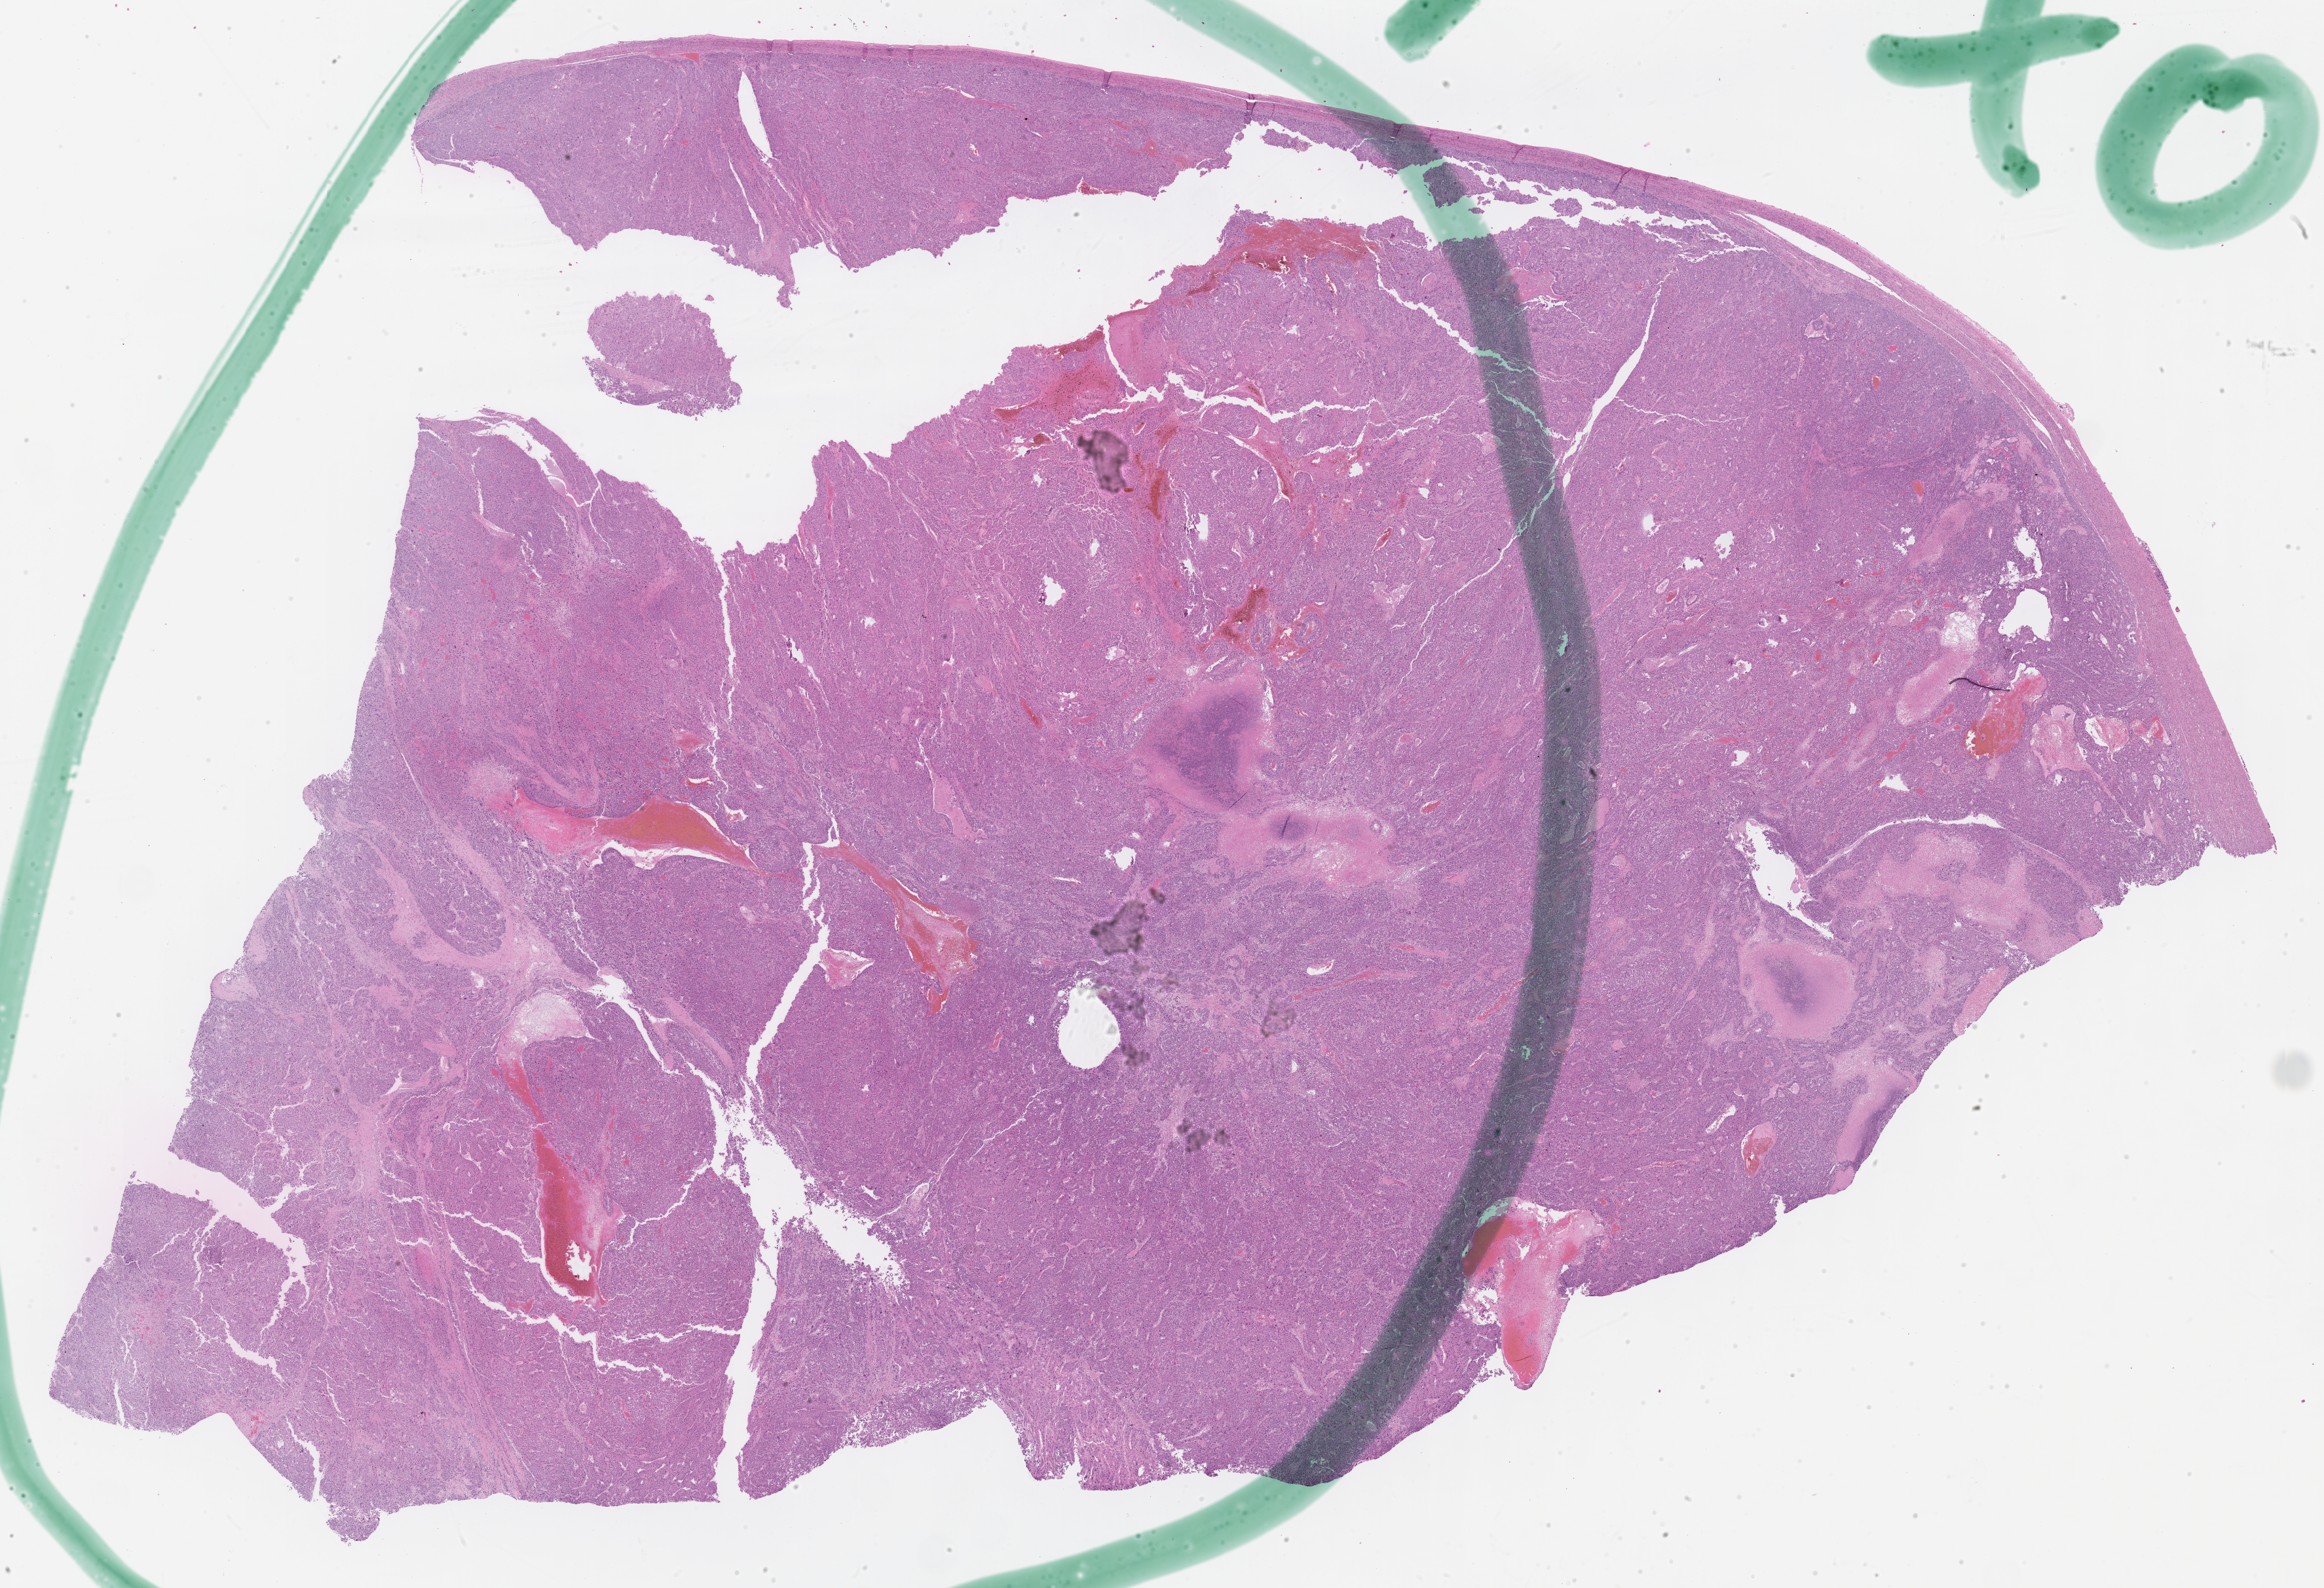
Whole-slide histology image, Hematoxylin and eosin (H&E) stained, whole scanned area (about 28.7 x 19.6 mm, acquisition: 40x scan) shown as a low-resolution overview. Formalin-fixed paraffin-embedded (FFPE) diagnostic section. Primary tumour sample from the liver. Patient: male, age at initial diagnosis 24 years. Histologic grade: G3 (poorly differentiated).
Histologic diagnosis: Hepatocellular carcinoma, NOS. AJCC pathologic stage: II (6th edition).